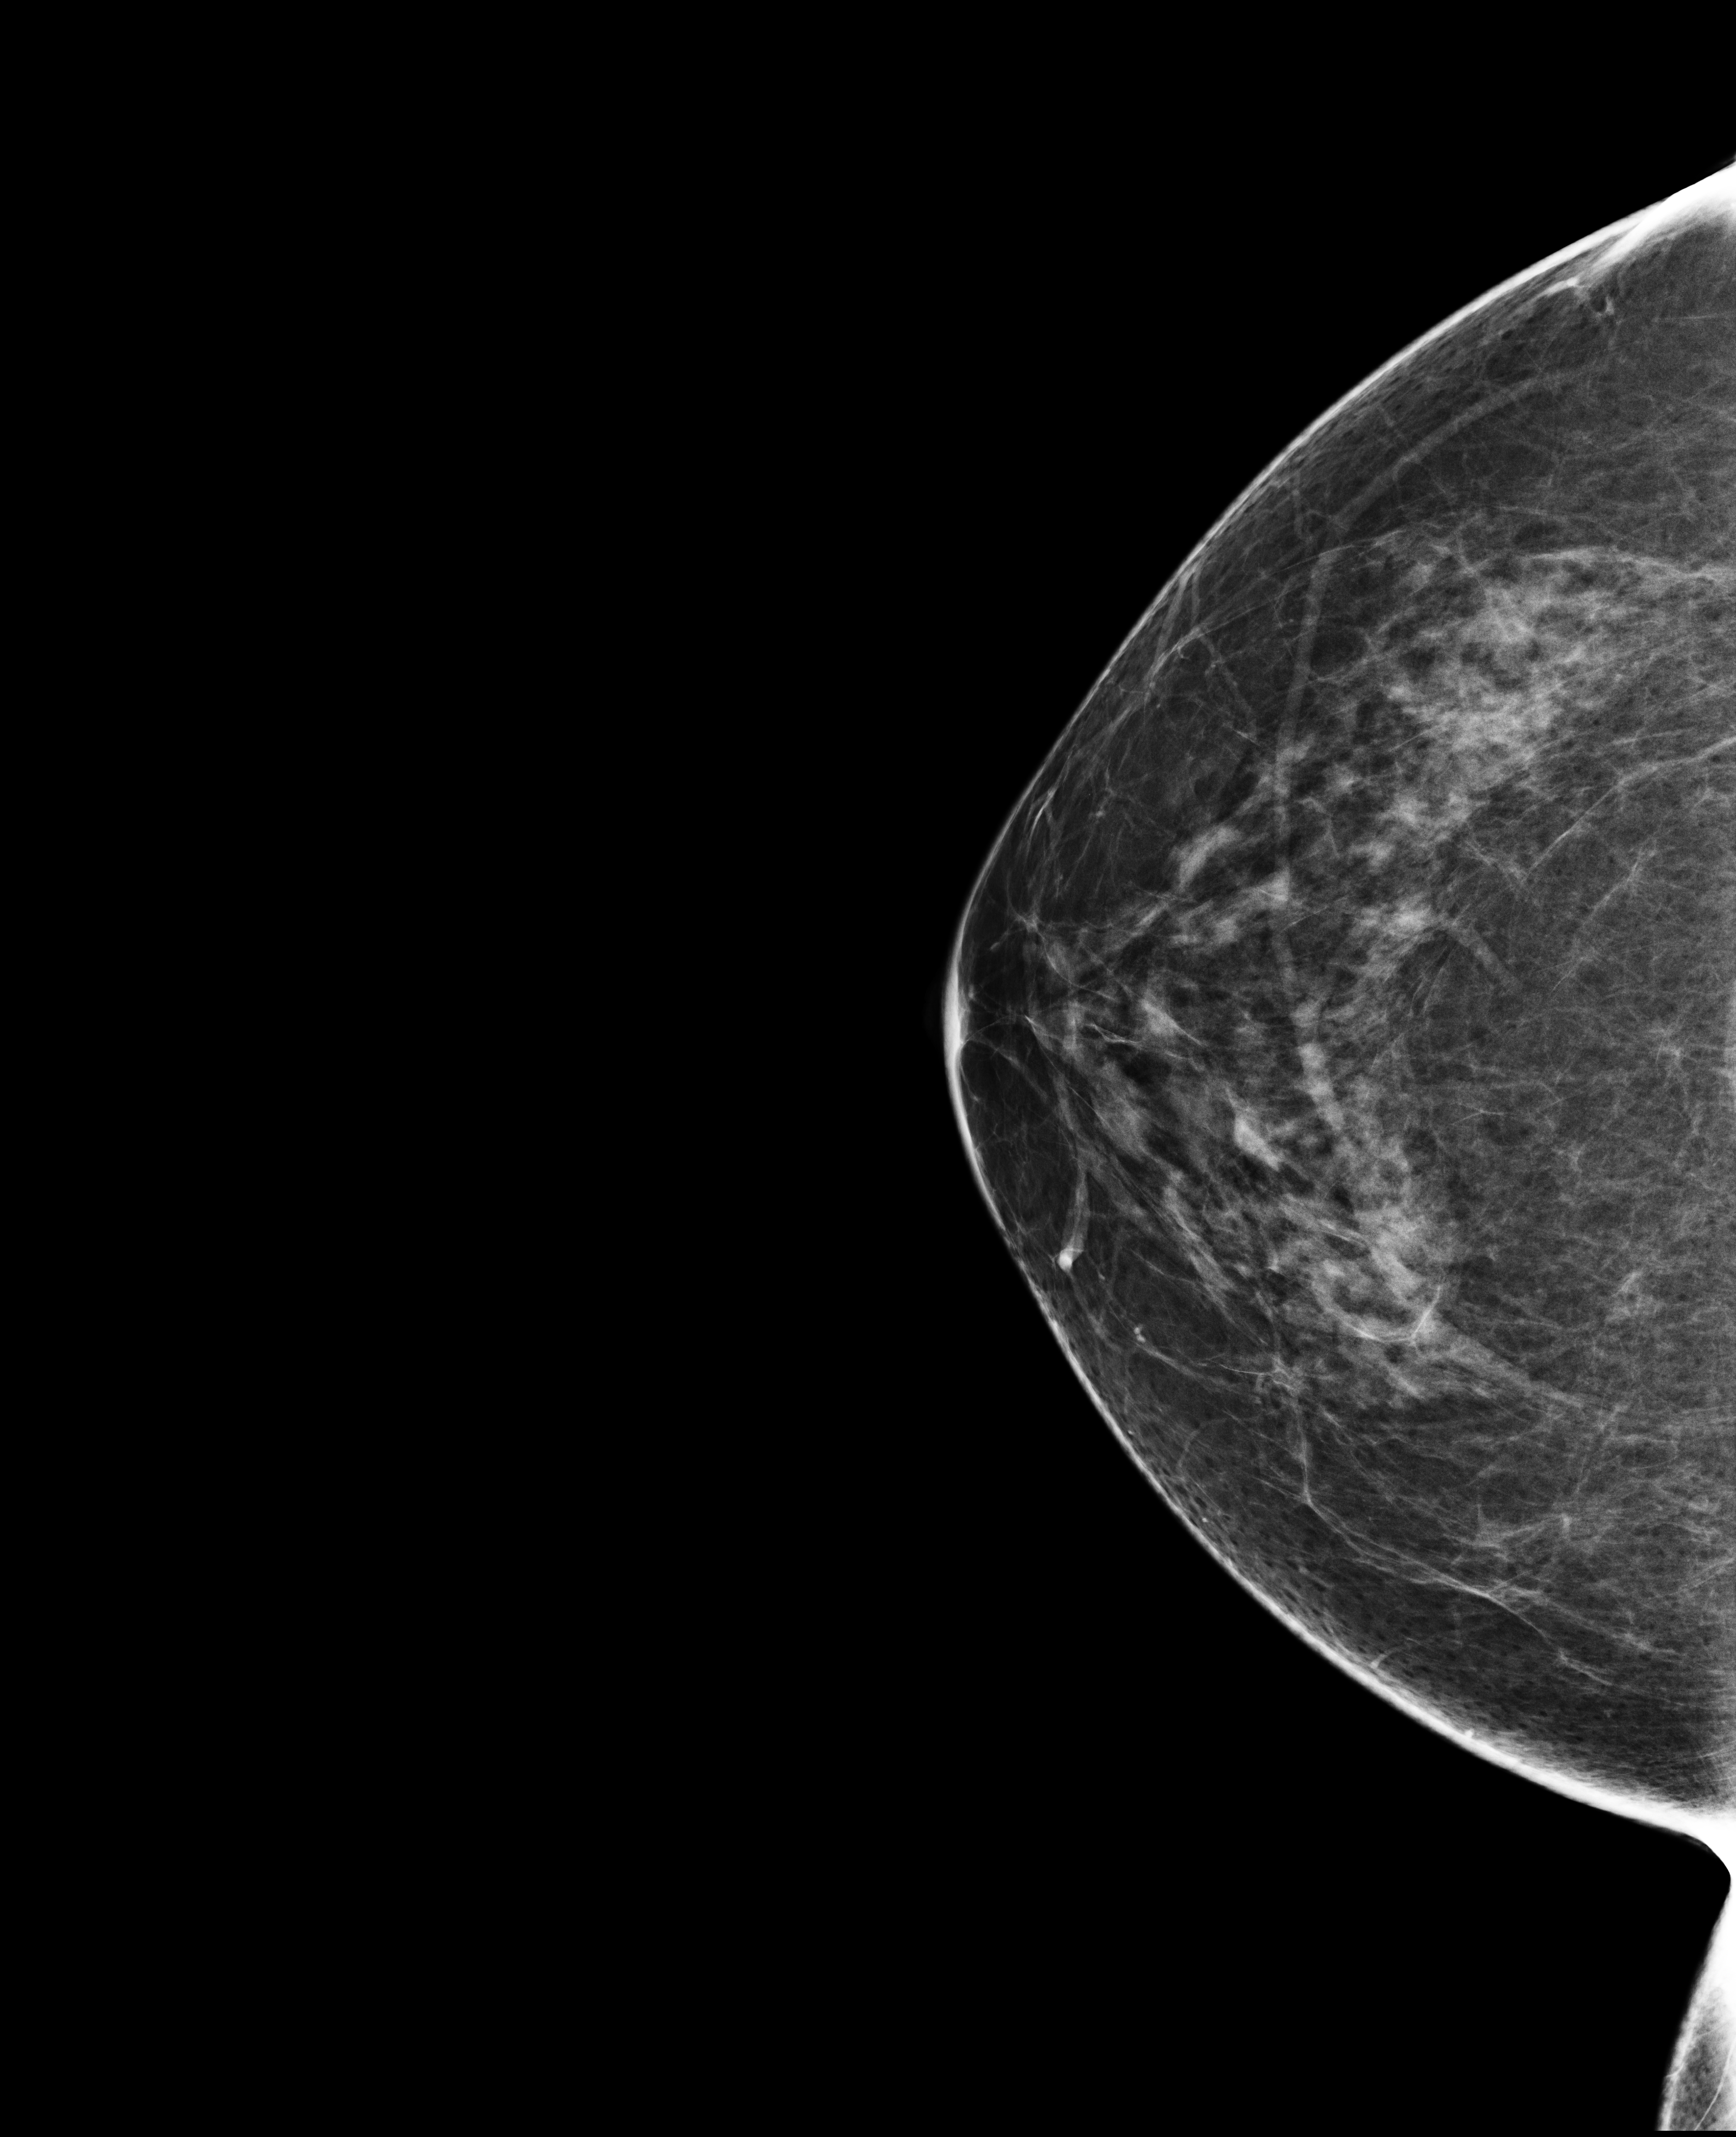
Annual screening mammography examination; compressed breast thickness 66 mm. Patient: female, 57 years.
Image type: full-field digital mammogram. Breast: right. Projection: CC view.